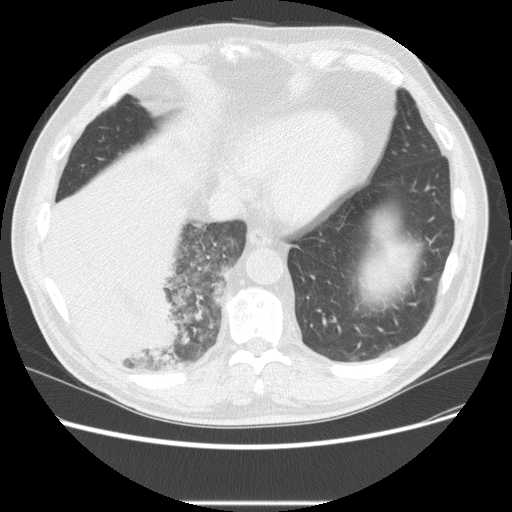
Low-dose screening chest CT, one axial slice. Slice 60 of 233 in the series (ordered by position). 120 kVp. Lung window (W 1500 / L -600 HU). 2.5 mm slice thickness. 512 × 512 image matrix, field of view 380 × 380 mm.
Structures marked on this image (outlined manually by an expert reader):
- lesion 3 (tumor, lower lobe of right lung): bounding box <48,195,183,371> (left, top, right, bottom; pixels)